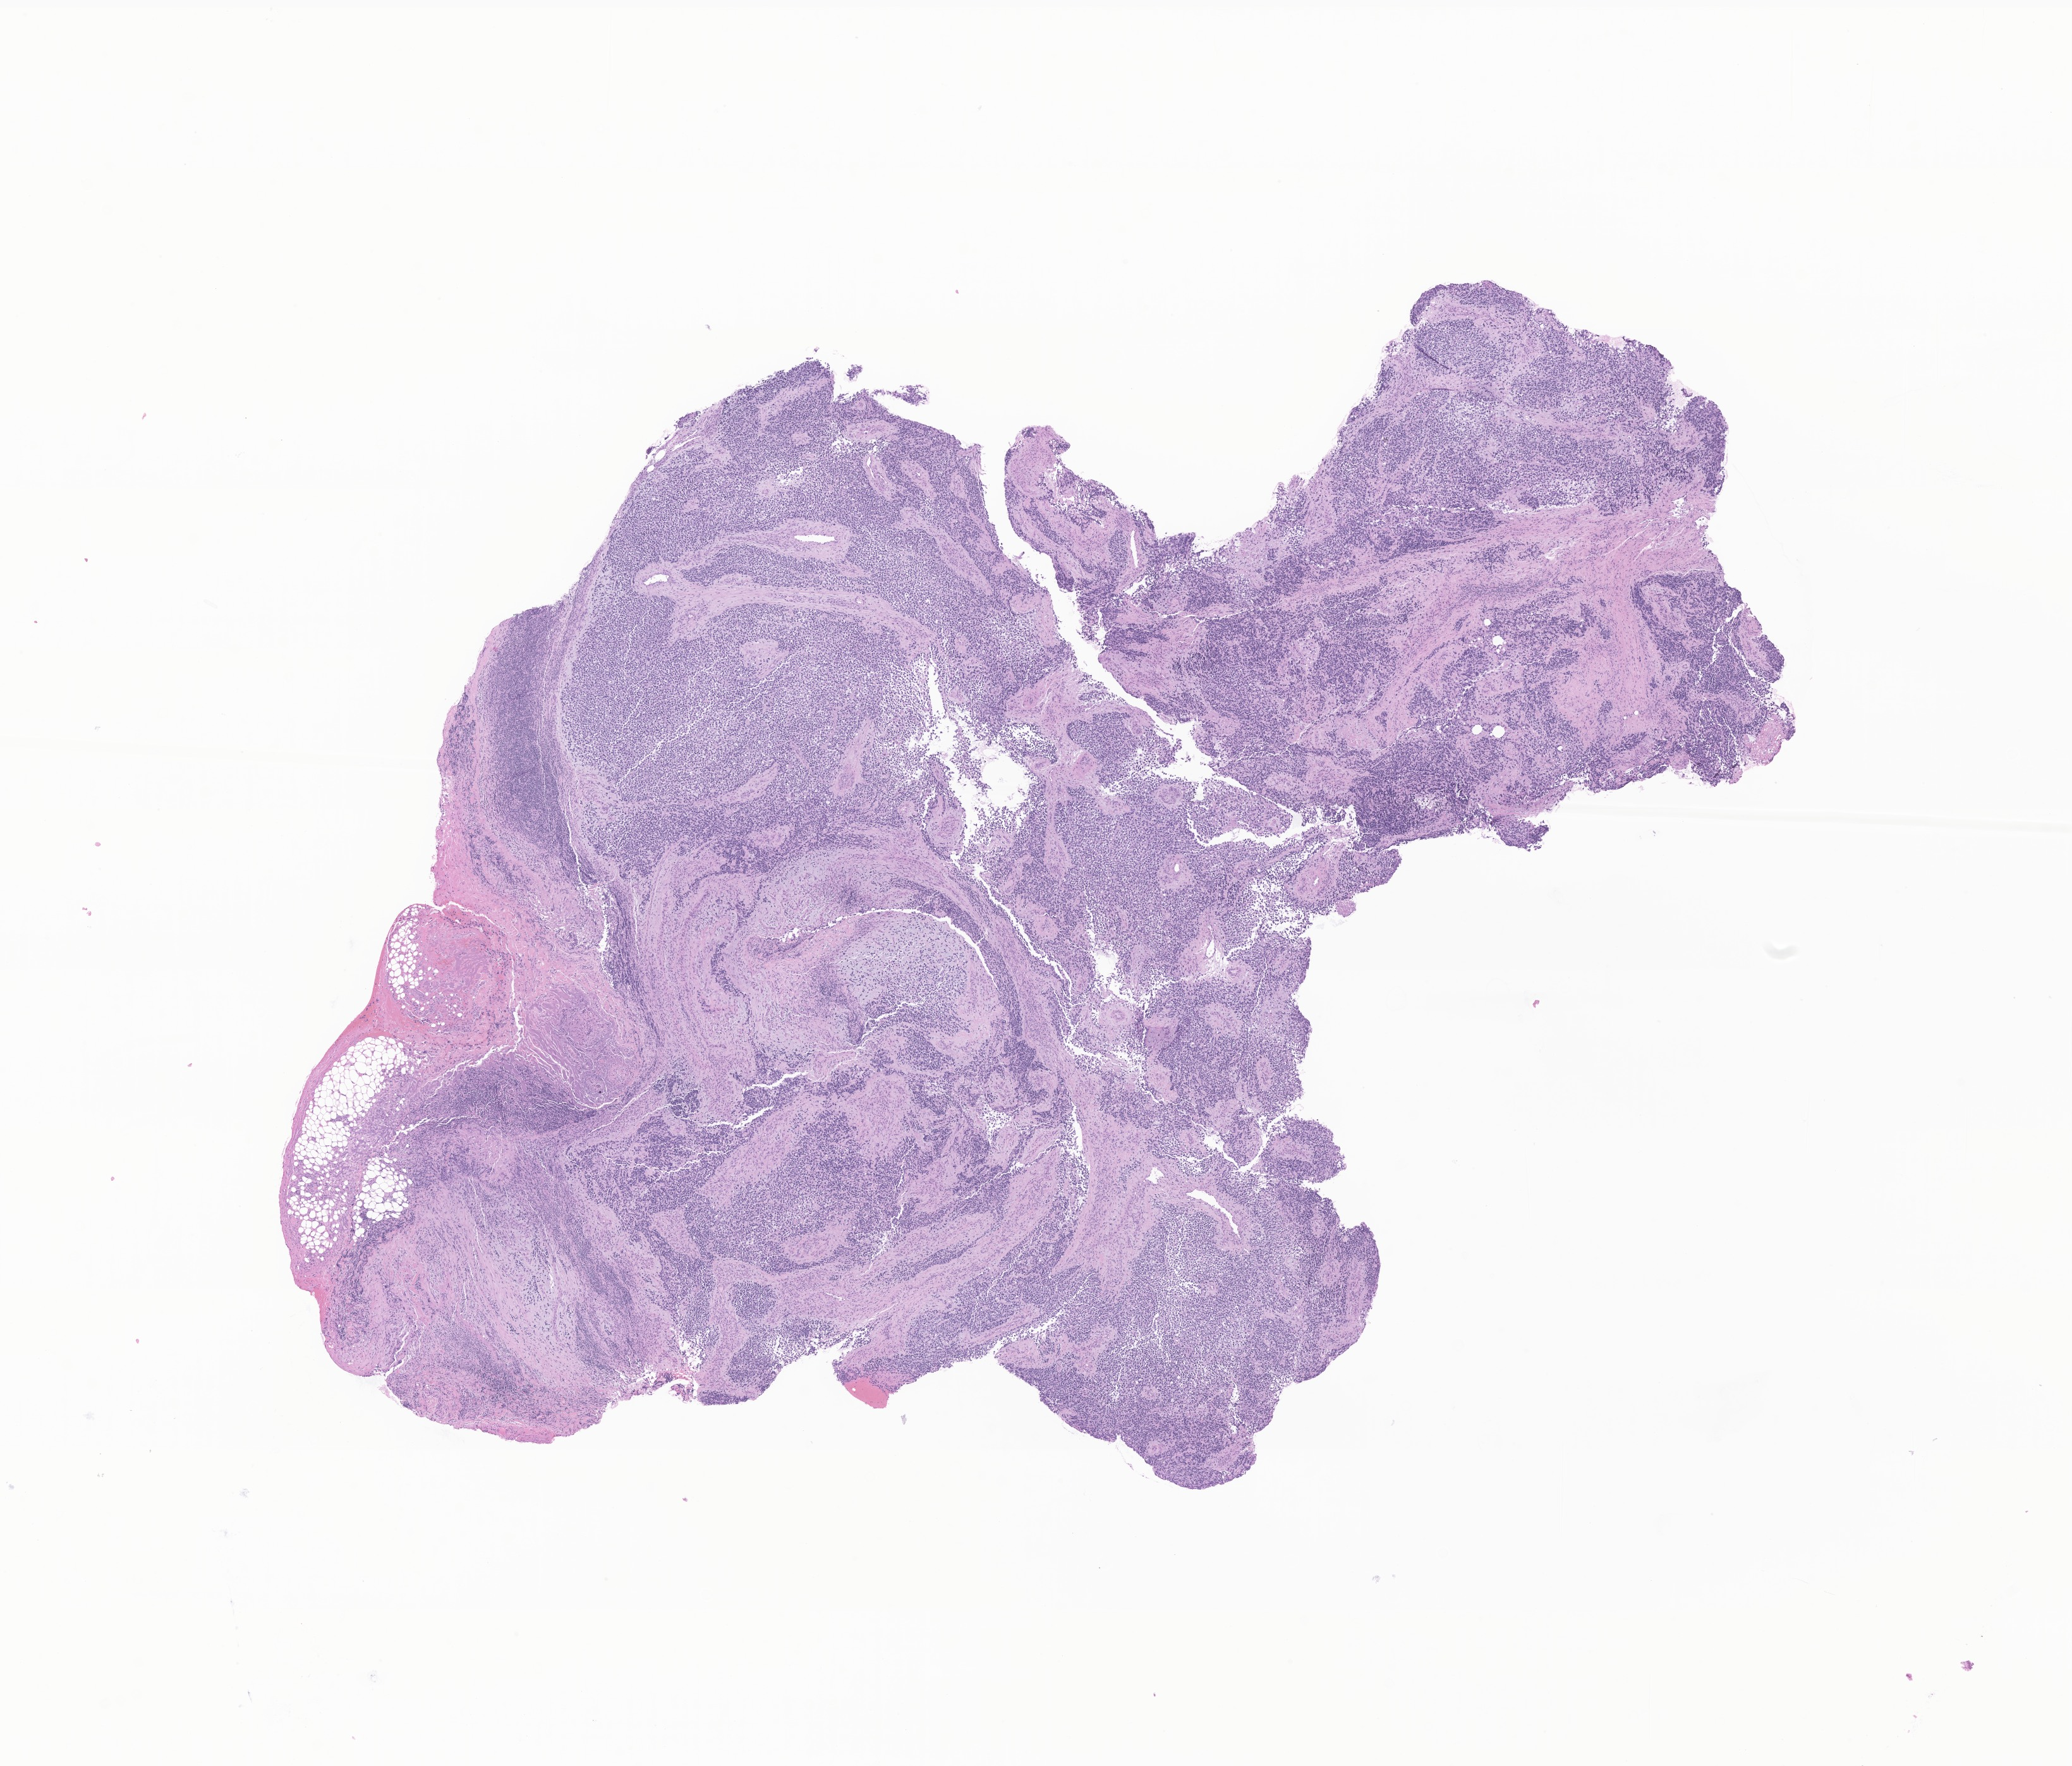
Digitized haematoxylin and eosin-stained section of tumor tissue from the pelvis, whole scanned area (about 13.8 x 11.8 mm) shown as a low-resolution overview. Formalin-fixed paraffin-embedded section. Patient: male, age 198 months (16 years 6 months).
* diagnosis (ICD-O-3 morphology term): Rhabdomyosarcoma, NOS